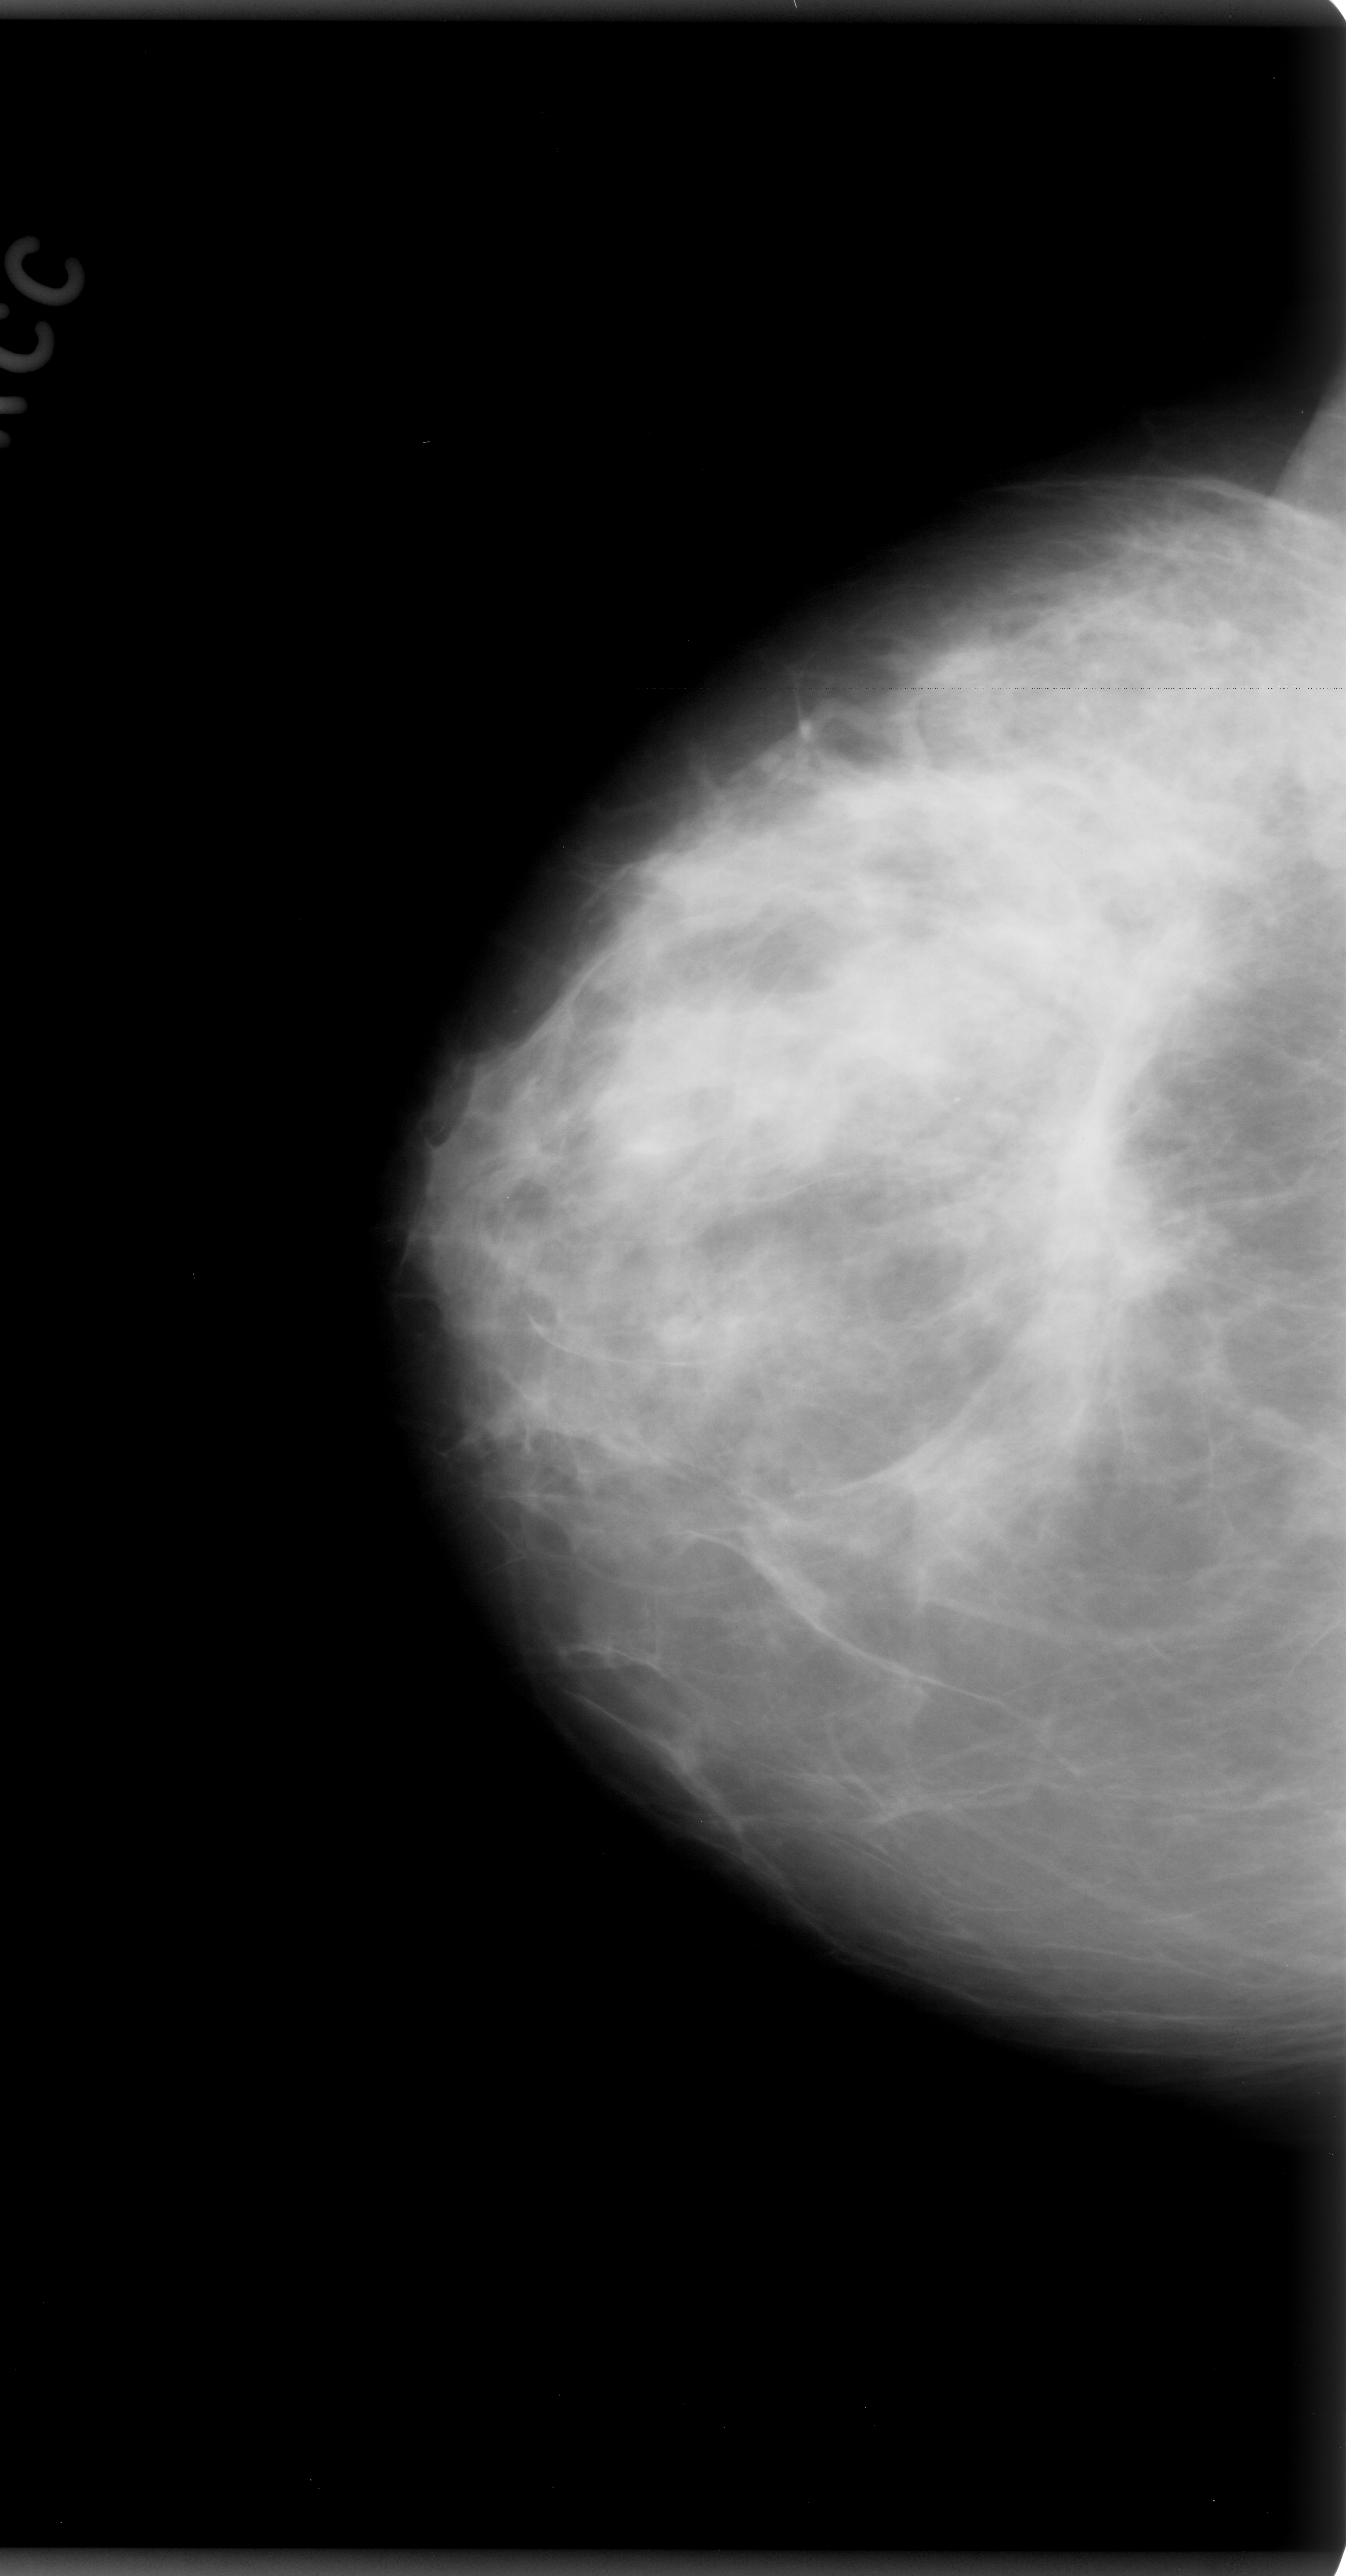
Scanned film-screen mammogram, right breast, CC view, BI-RADS breast density category 3 (scale 1–4).
Abnormality record for this image: mass, shape architectural distortion, margins spiculated; BI-RADS assessment category 5; pathology (as recorded): malignant.